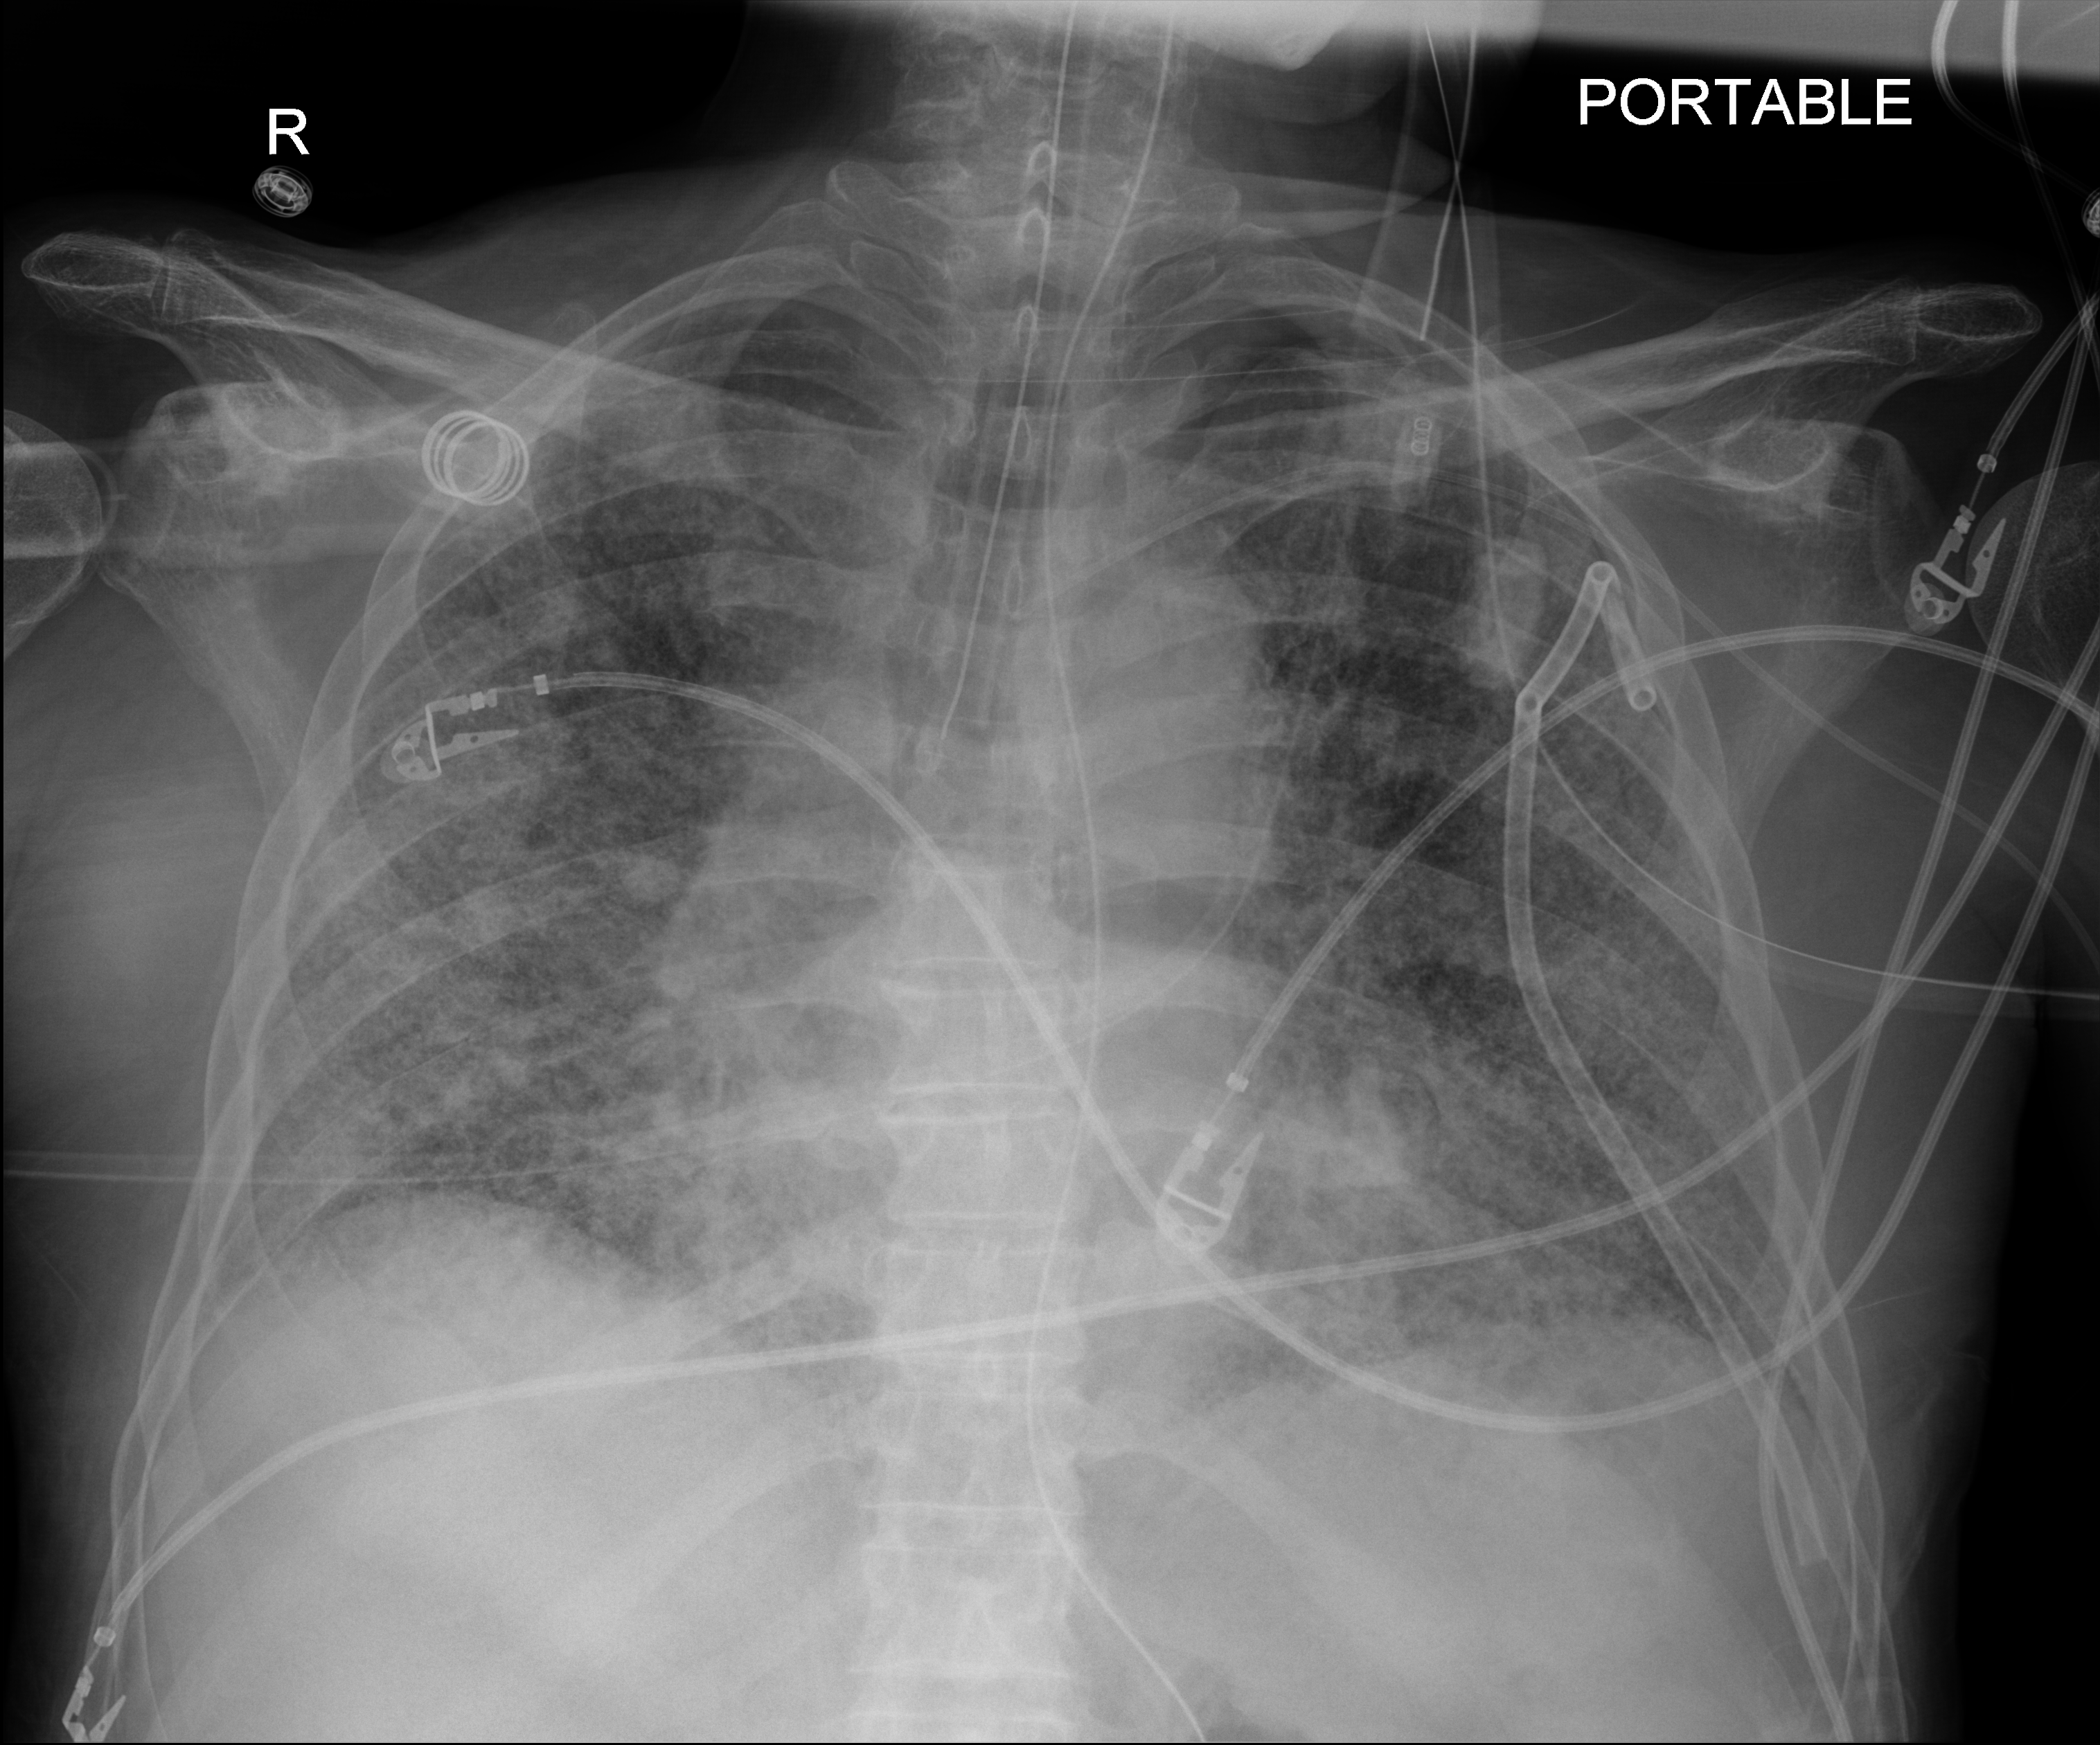
Chest radiograph (digital radiography). Male patient hospitalised with COVID-19, age 60–74 years.
From the hospital-stay record, not from the radiograph (when in the stay this image was taken is not recorded): mechanically ventilated during this hospital stay: yes; admitted to intensive care during this hospital stay: yes.